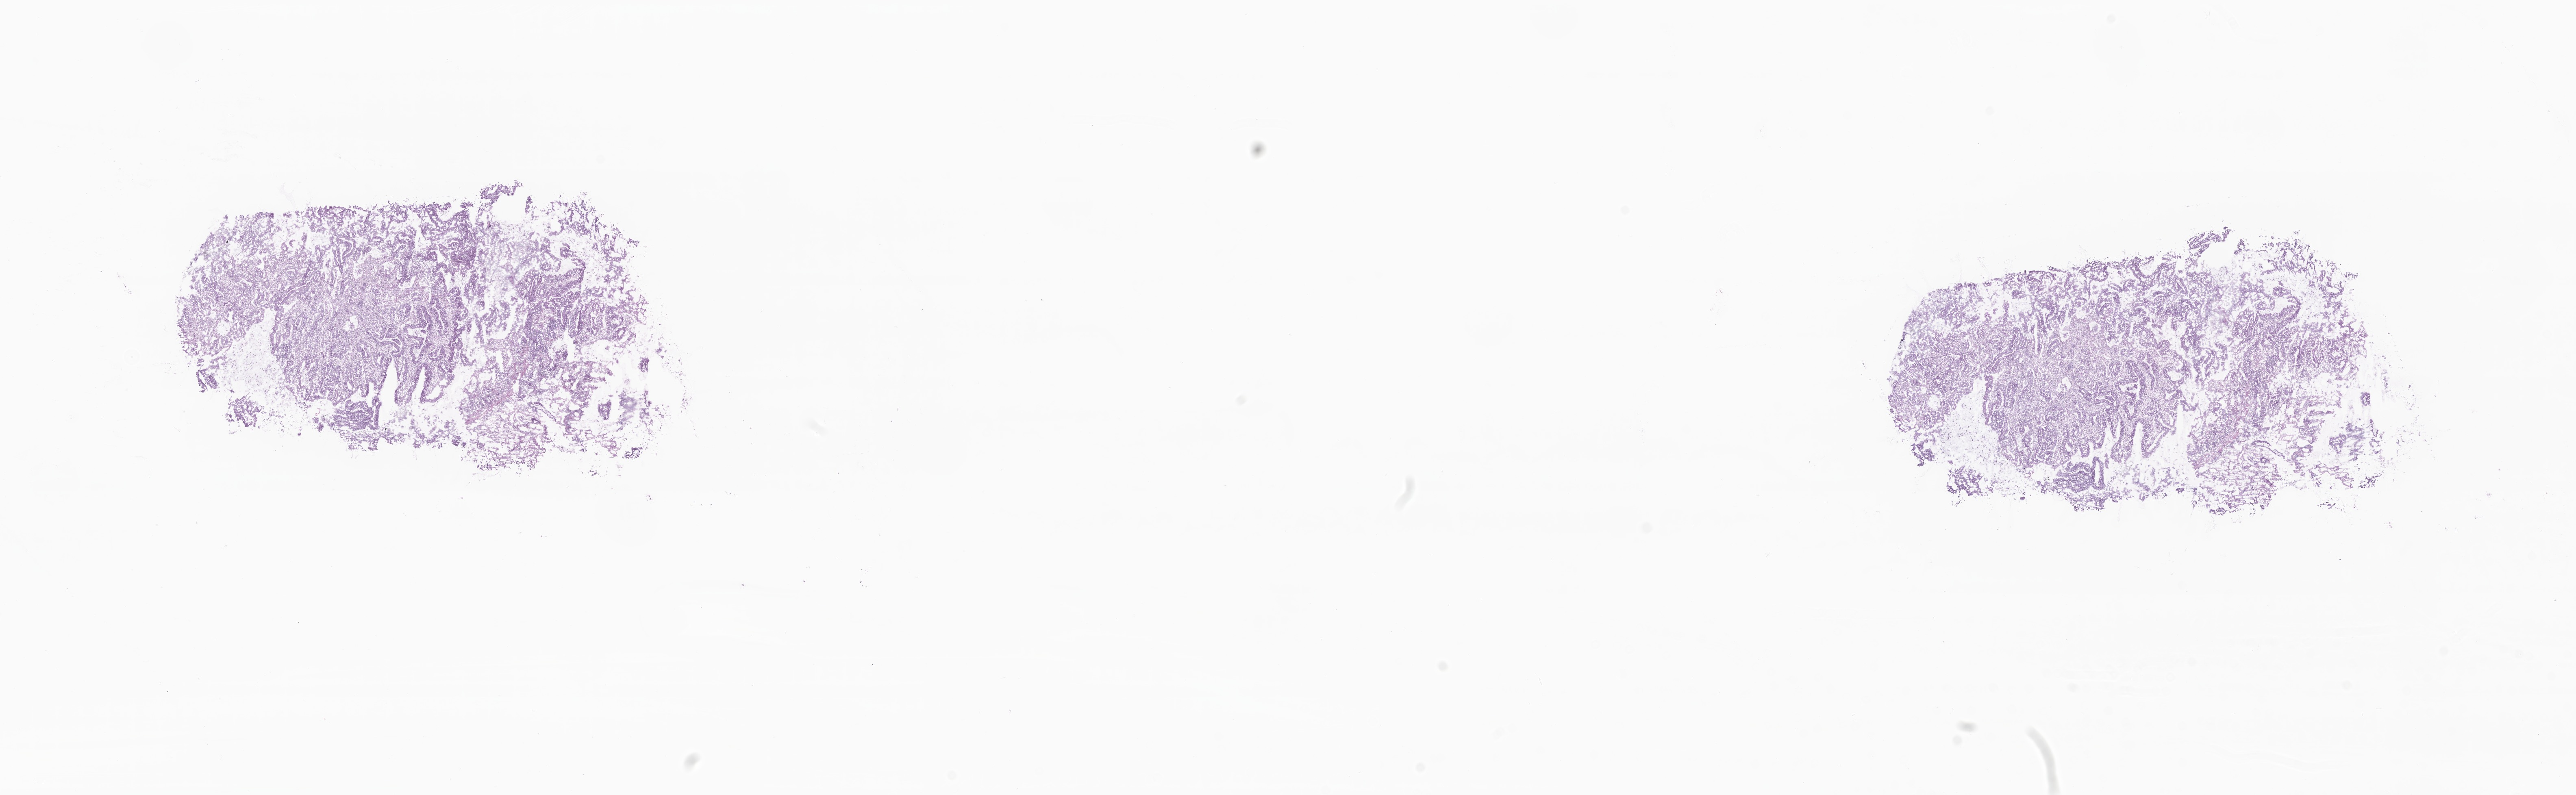
Digitized hematoxylin and eosin (H&E)-stained section, low-resolution overview of the scanned area, about 26.7 x 8.2 mm; frozen section; specimen: primary tumor; anatomic site: transverse colon. Patient sex: female. Pathologist review of this section (percent, as recorded): tumor cells 100%, tumor nuclei 55%, stromal cells 0%, necrosis 0%, normal cells 0%. Infiltration values recorded for this section: lymphocyte infiltration 0%, monocyte infiltration 0%, neutrophil infiltration 0%.
Diagnosis: Adenocarcinoma, NOS.